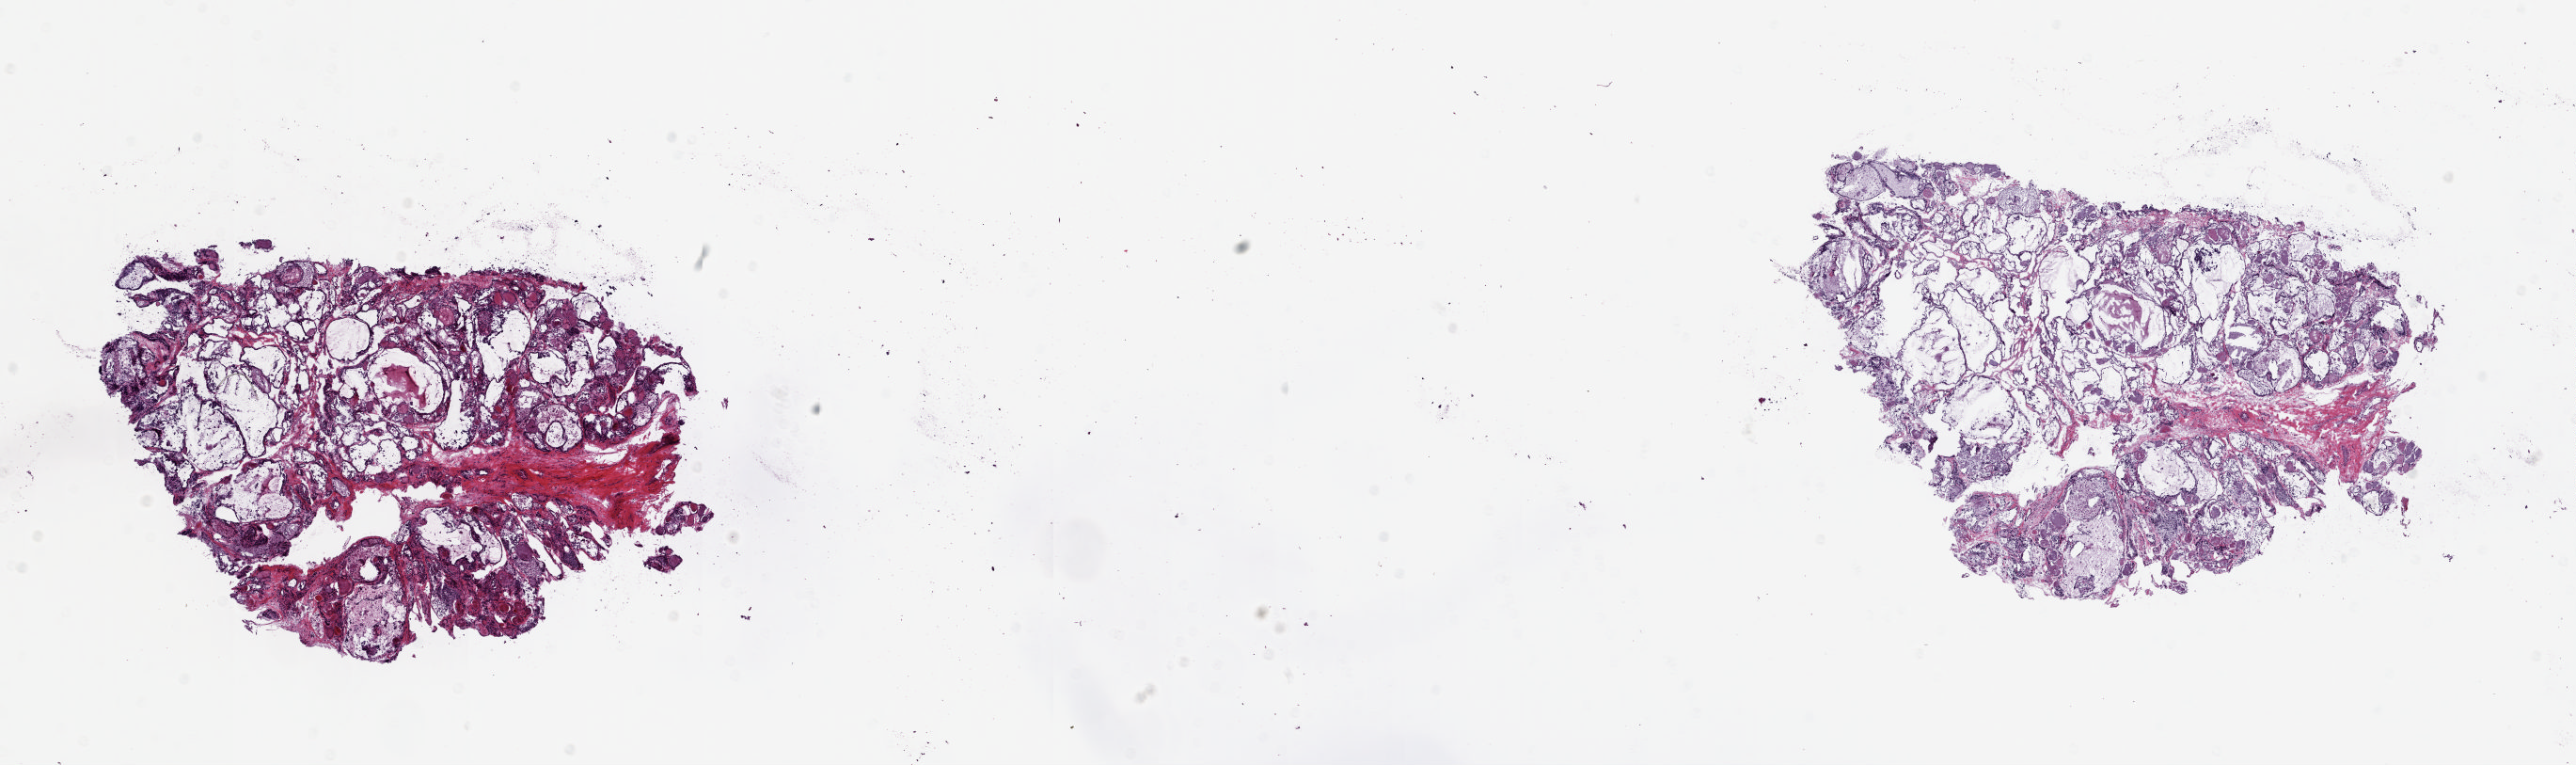
Digitized H&E-stained tissue section (whole slide) — a low-resolution overview of the entire scanned area, about 21.8 x 6.5 mm (acquisition: 20x scan), frozen section from the top of the tissue portion, solid tissue normal (non-tumour tissue) sample from the thyroid. Patient: female, age at initial diagnosis 71 years. Composition of this section per pathologist review: tumour cells 0%, tumour nuclei 0%, normal cells 100%, stromal cells 0%, necrosis 0%. Inflammatory infiltration, as recorded: lymphocyte infiltration 0%, monocyte infiltration 2%, neutrophil infiltration 0%.
• this section: solid tissue normal (non-tumour) sample from the same patient
• patient diagnosis: Papillary carcinoma, follicular variant (thyroid gland)